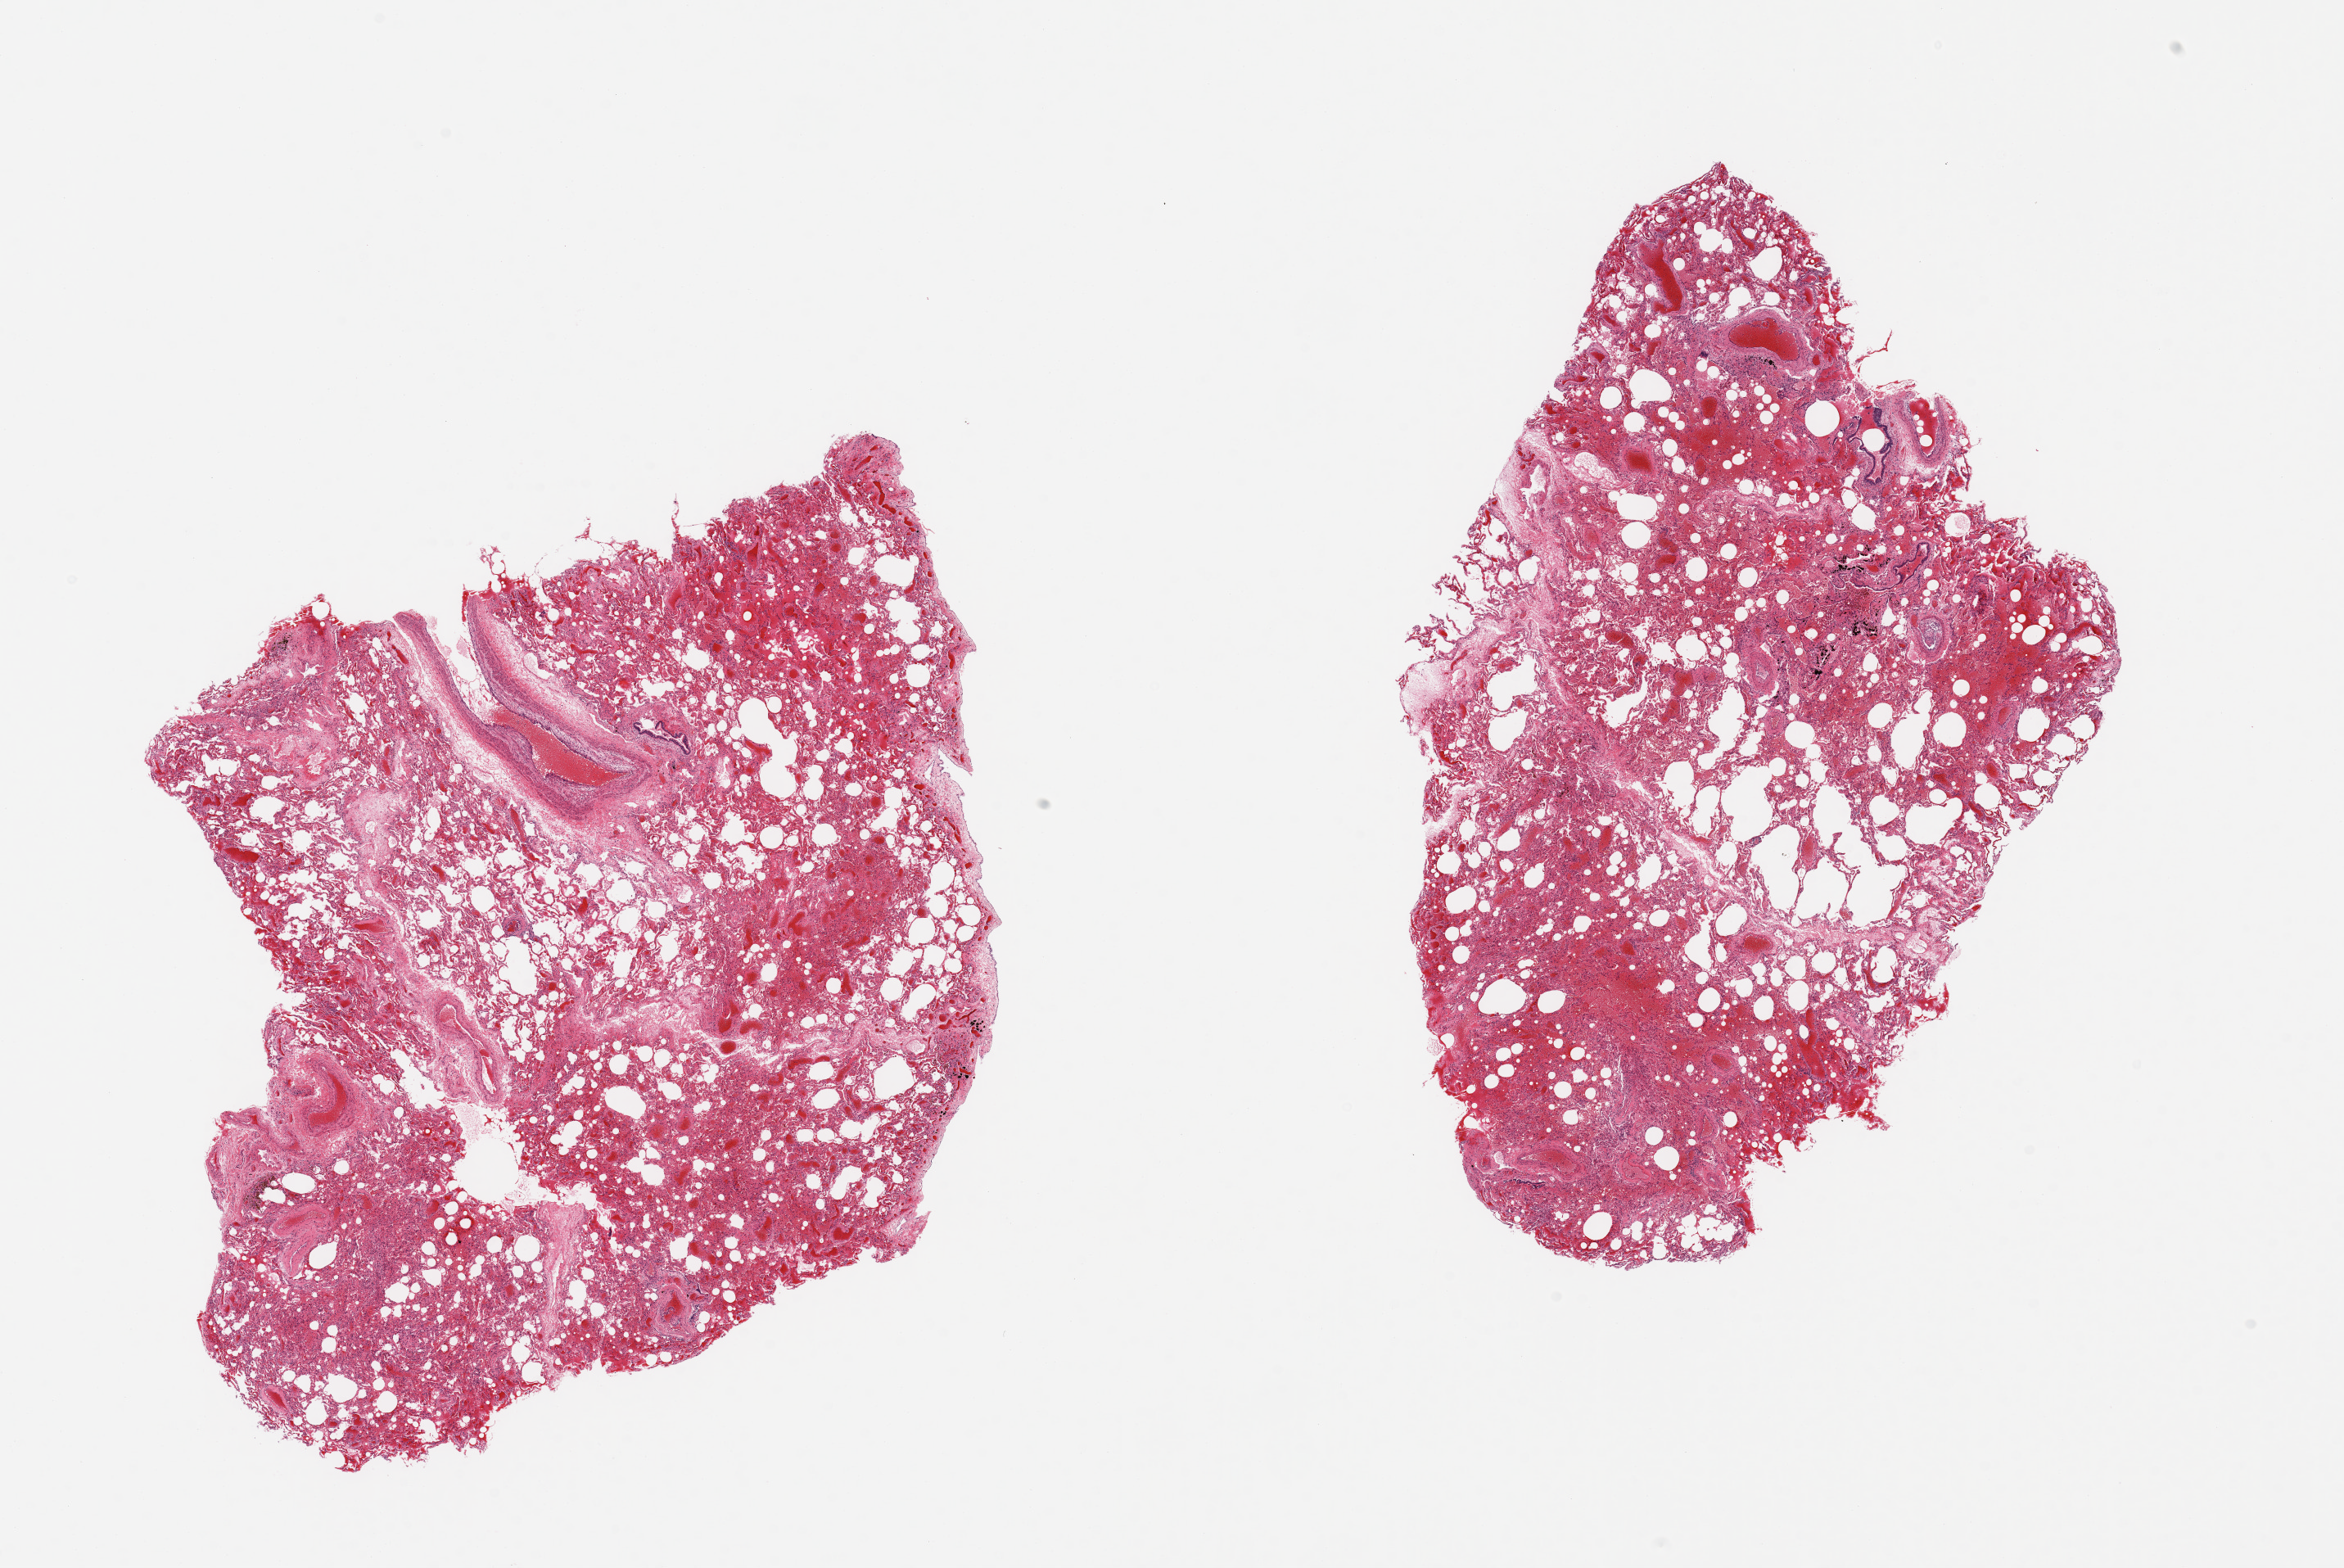
Whole-slide image, hematoxylin and eosin (H&E) stain — shown as a low-resolution overview of the whole scanned area (about 22.6 x 15.1 mm); PAXgene-fixed paraffin-embedded (PFPE) section; section of lung (target tissue); donor tissue sample.
Review note (as recorded): 2 pieces; patchy moderate alveolar hemorrhage; foci of dark pigment; mild emphysema.